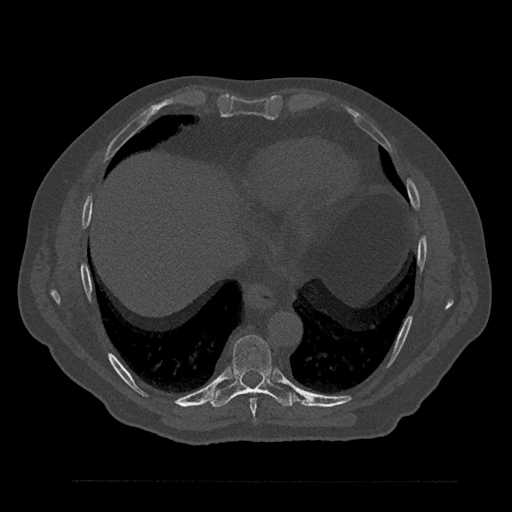
CT including the spine, one axial slice; position 418 of 797 along the scan axis; reconstruction kernel Br40s/3; bone window (W 1800 / L 400 HU); 0.5 mm slice thickness; 512 × 512 image matrix, field of view 430 × 430 mm. Male patient, age 61 years. Case-level facts recorded for this patient, not image findings: primary cancer: prostate.
Outlined on this slice (semi-automatic segmentation, software-assisted and operator-edited):
- T8 vertebra: bounding box <250,398,257,423> (left, top, right, bottom; pixels)
- T9 vertebra: <210,335,296,408>